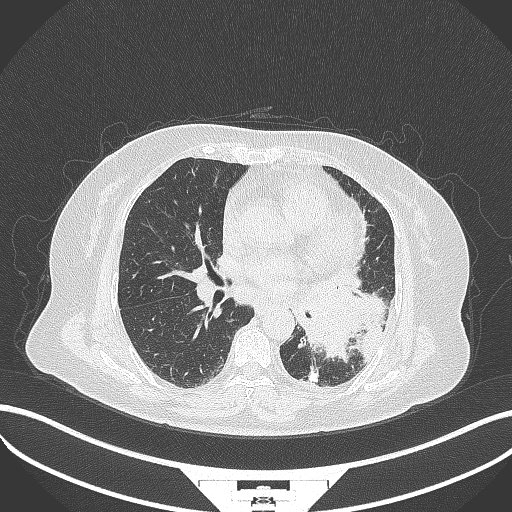
Chest CT, one axial slice; position 172 of 322 along the scan axis; 120 kVp; lung window (W 1500 / L -600 HU); 1 mm slice thickness; 512 × 512 image matrix. Patient: female, 69 years. From the clinical record (not read from this slice): clinical TNM (as recorded): T2b N3 M1.
Structures marked on this image (rectangle marked by the reading radiologist):
- lung tumour (recorded histology: adenocarcinoma): box from (x=297, y=271) to (x=384, y=358) px